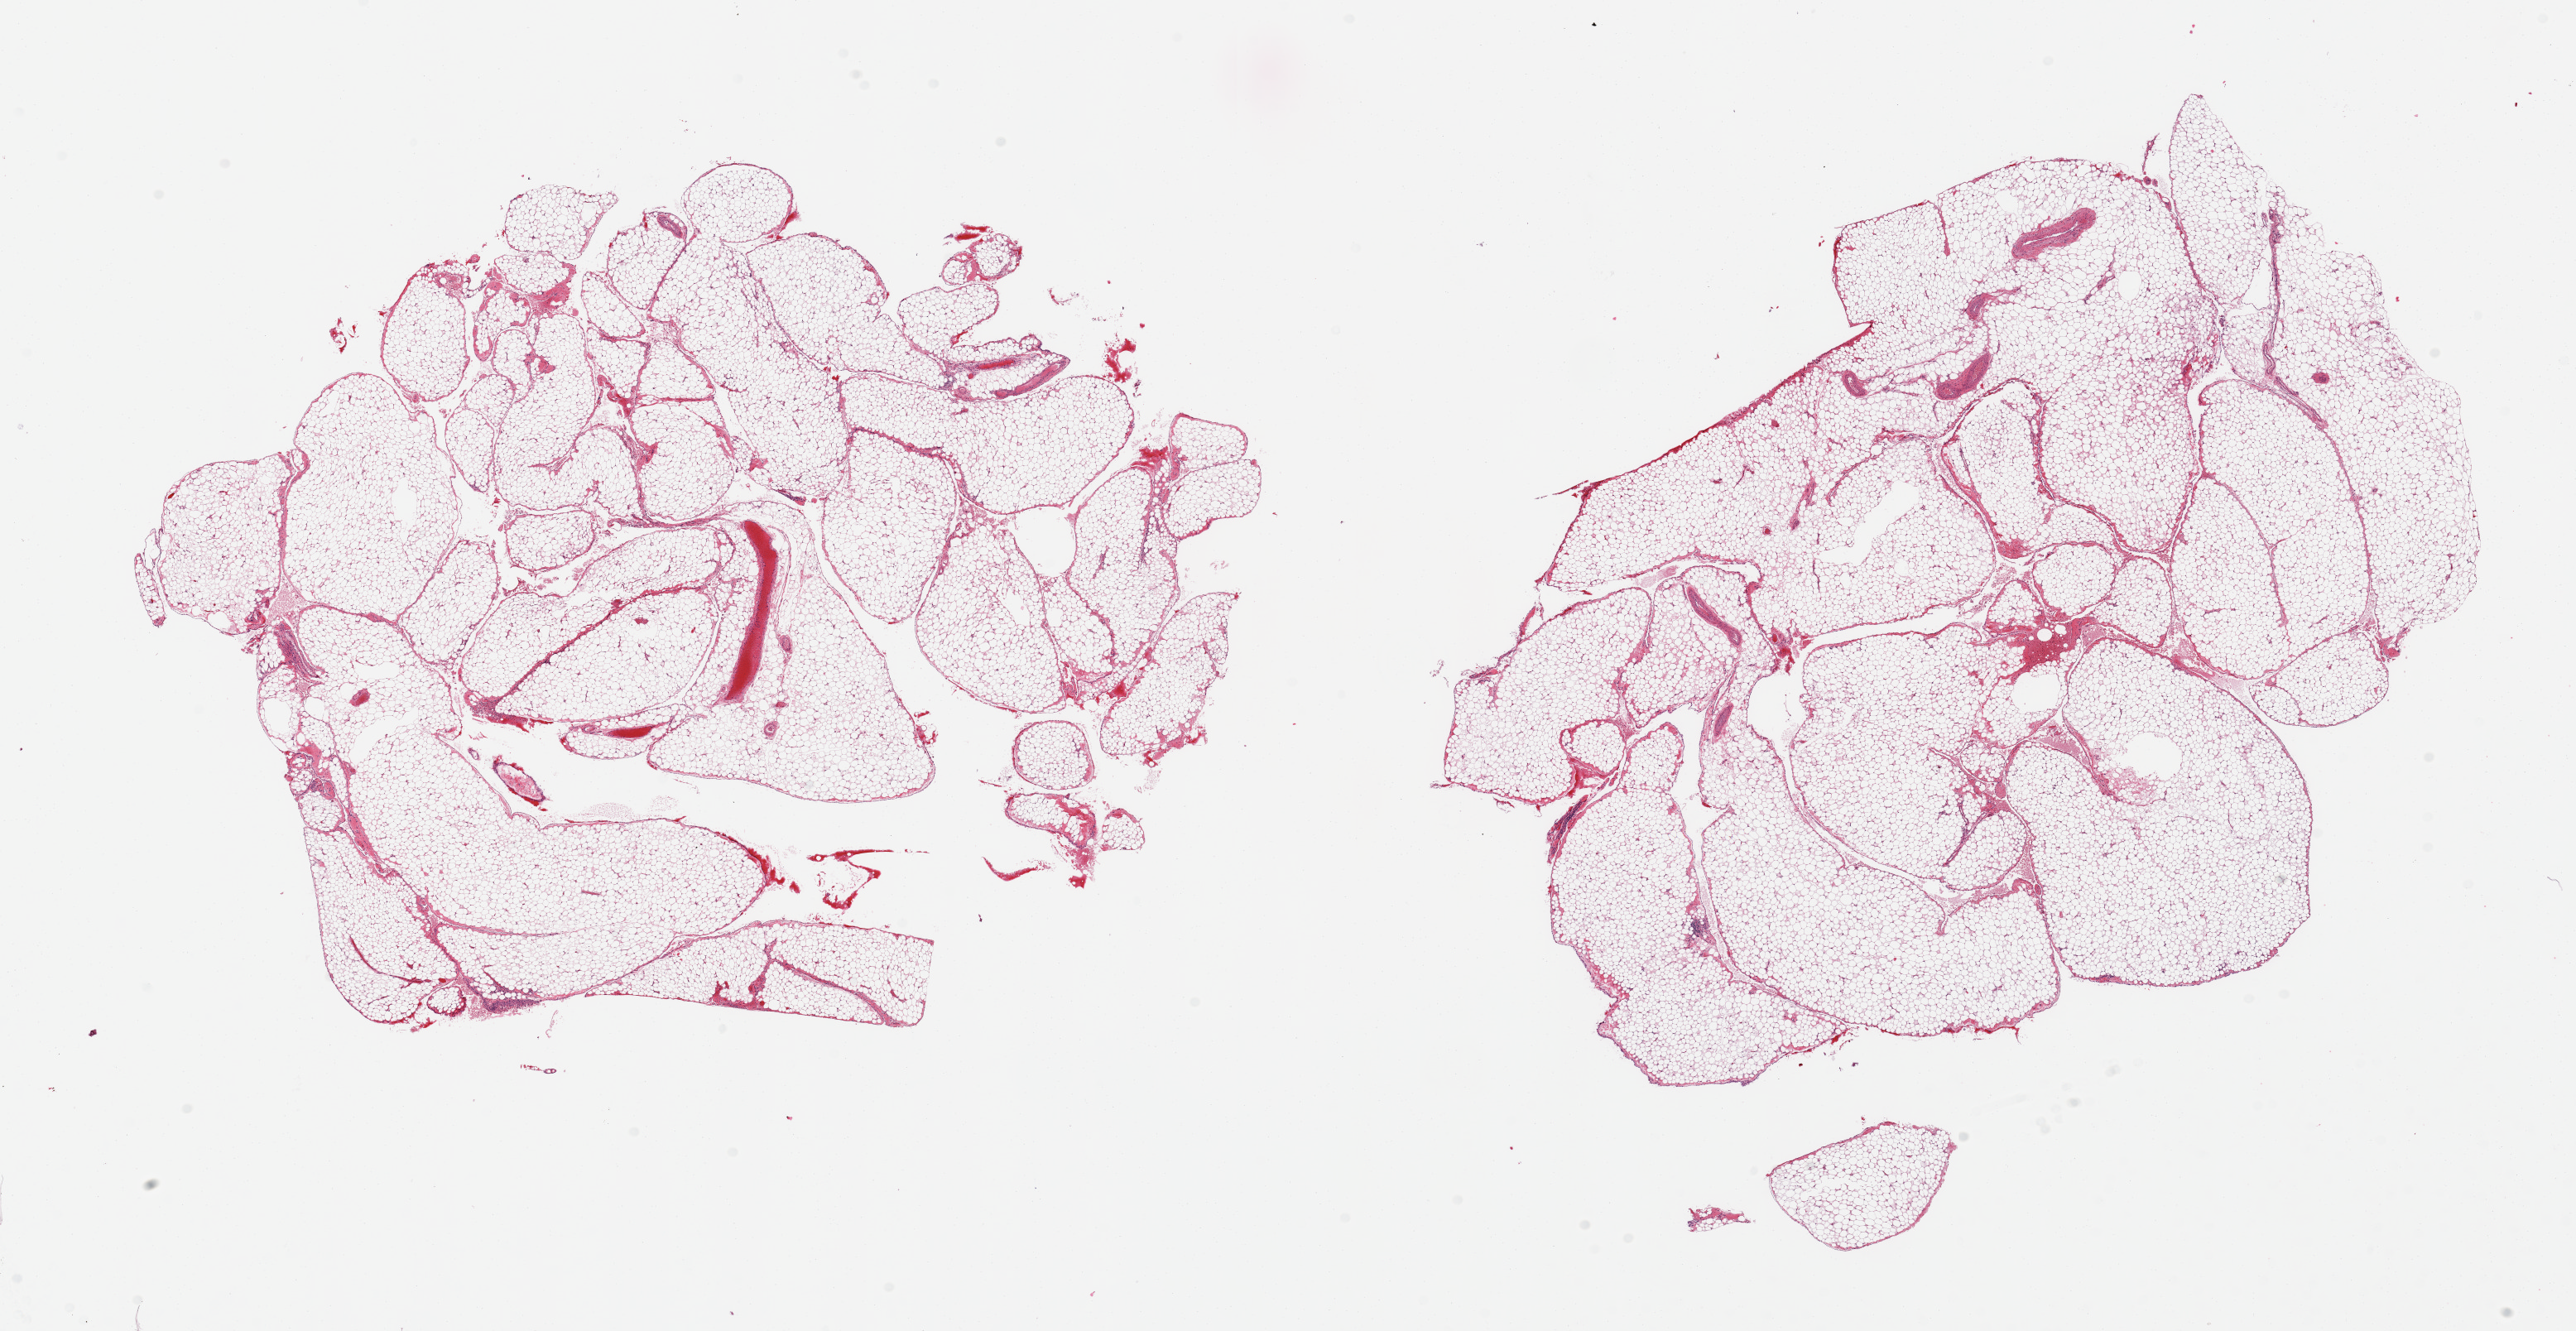
Hematoxylin and eosin (H&E) whole-slide image, shown as a low-resolution overview of the whole scanned area (about 24.6 x 12.7 mm, from a 20x scan); PAXgene-fixed paraffin-embedded (PFPE) section; sampled site (target tissue): omentum; tissue donor sample. Male donor.
• review note (as recorded): 2 pieces, ~5-10% fascia/vascular elements